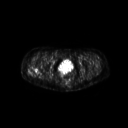
FDG PET of an extremity soft-tissue mass (from a PET/CT study), one axial slice. Slice 50 of 267 in the series (ordered by position). 3.27 mm slice thickness. 128 × 128 image matrix. Female patient, age 57 years. From the clinical record (not read from this slice): histological type: epithelioid sarcoma with vascular differentiation; site of the primary tumour: right buttock.
Outlined on this slice (expert contour drawn on MRI and transferred to this co-registered scan by the dataset authors):
- gross tumour volume (mass): bounding box (x1, y1, x2, y2) in pixels: (25, 65, 43, 79)